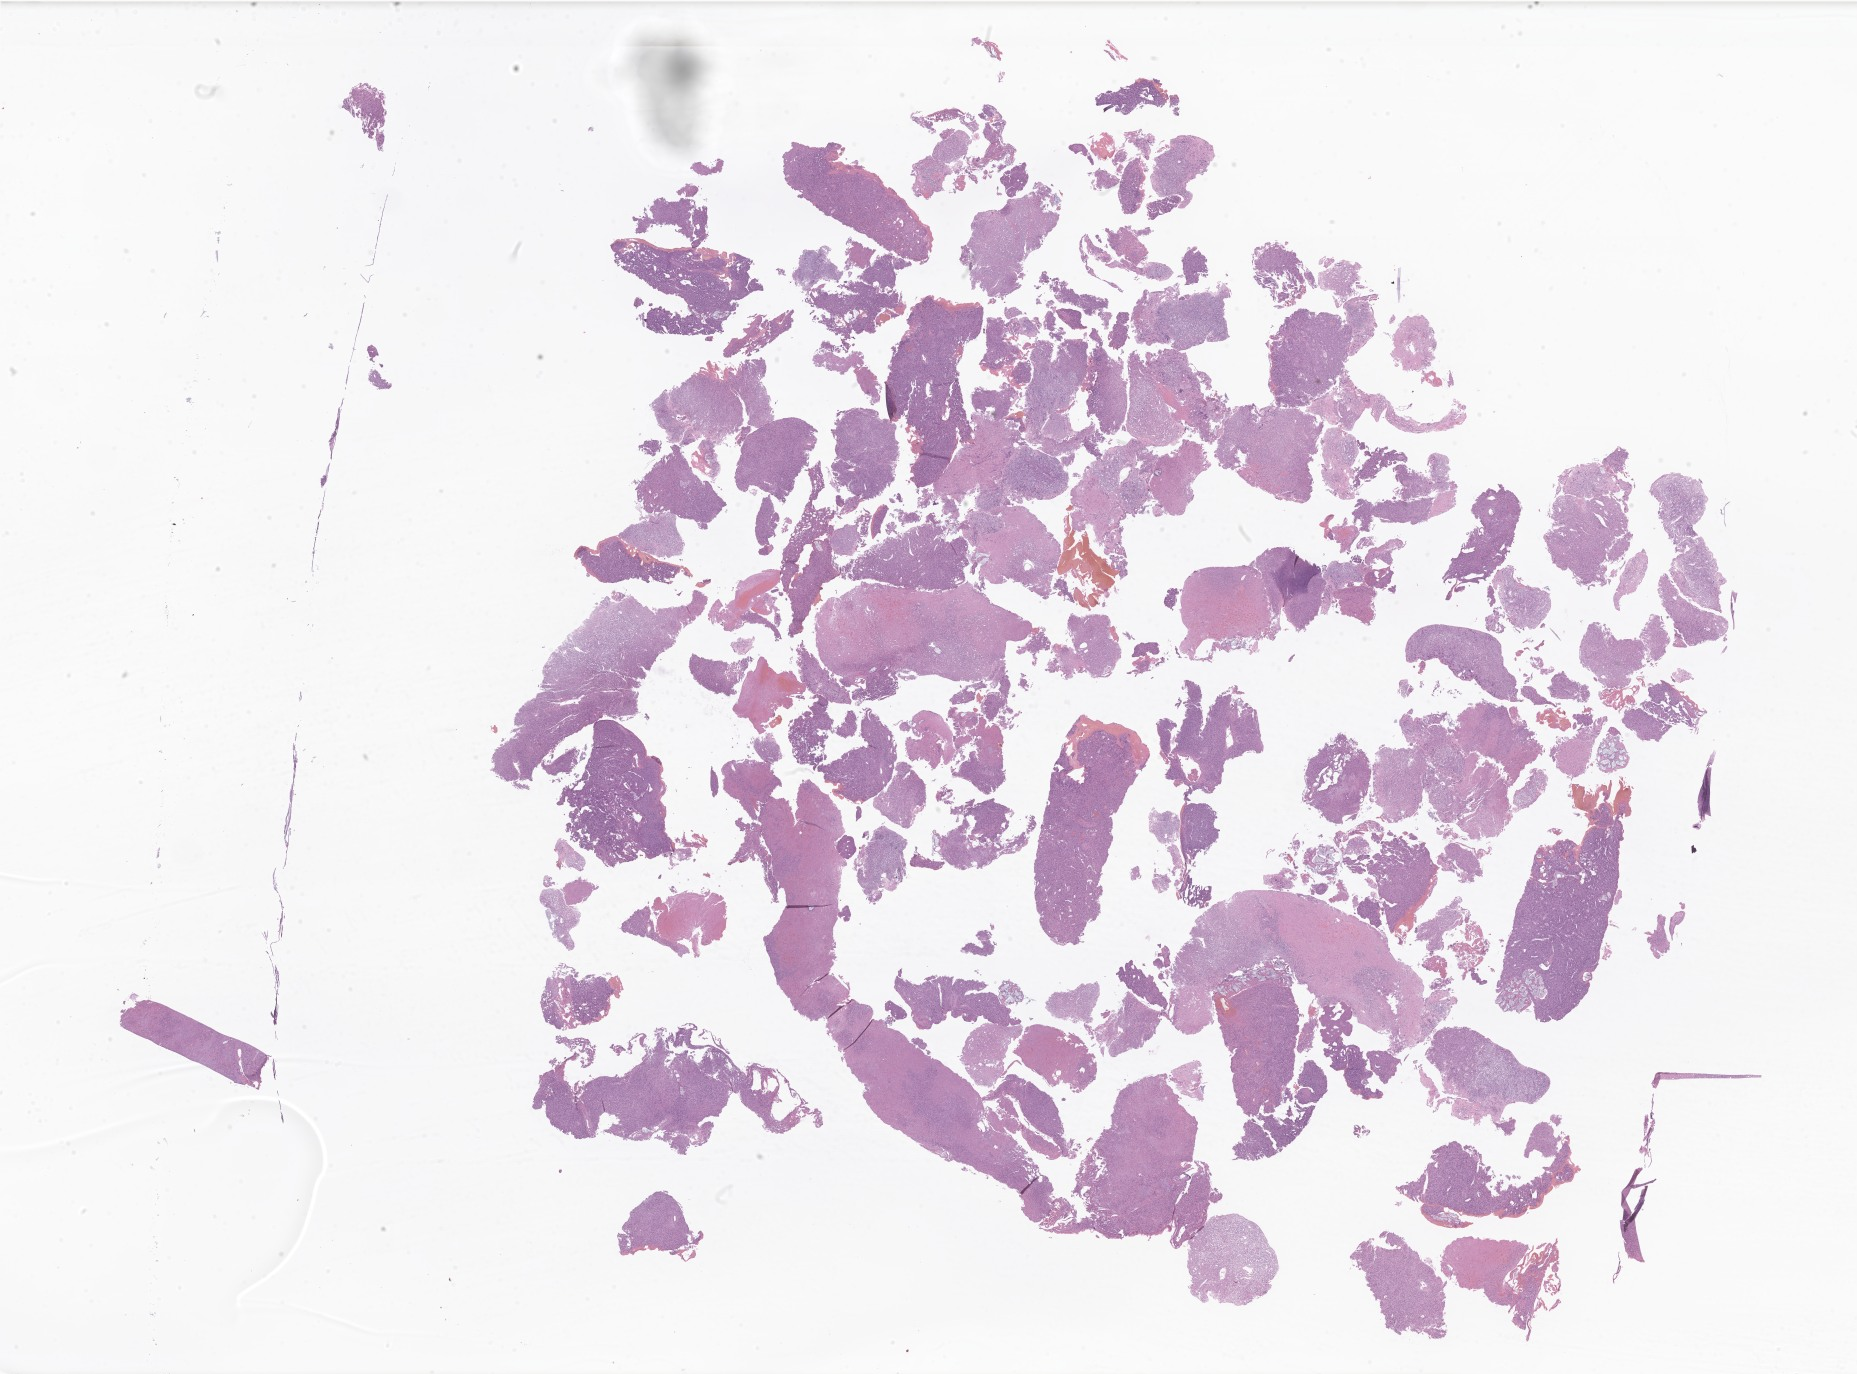
Digitized H&E-stained section of tumor tissue from the brain, a low-resolution overview of the entire scanned area, about 31.3 x 23.2 mm. Formalin-fixed paraffin-embedded section. Female patient, age 206 months (17 years 2 months).
- diagnosis: Solitary fibrous tumor/Hemangiopericytoma, grade 1